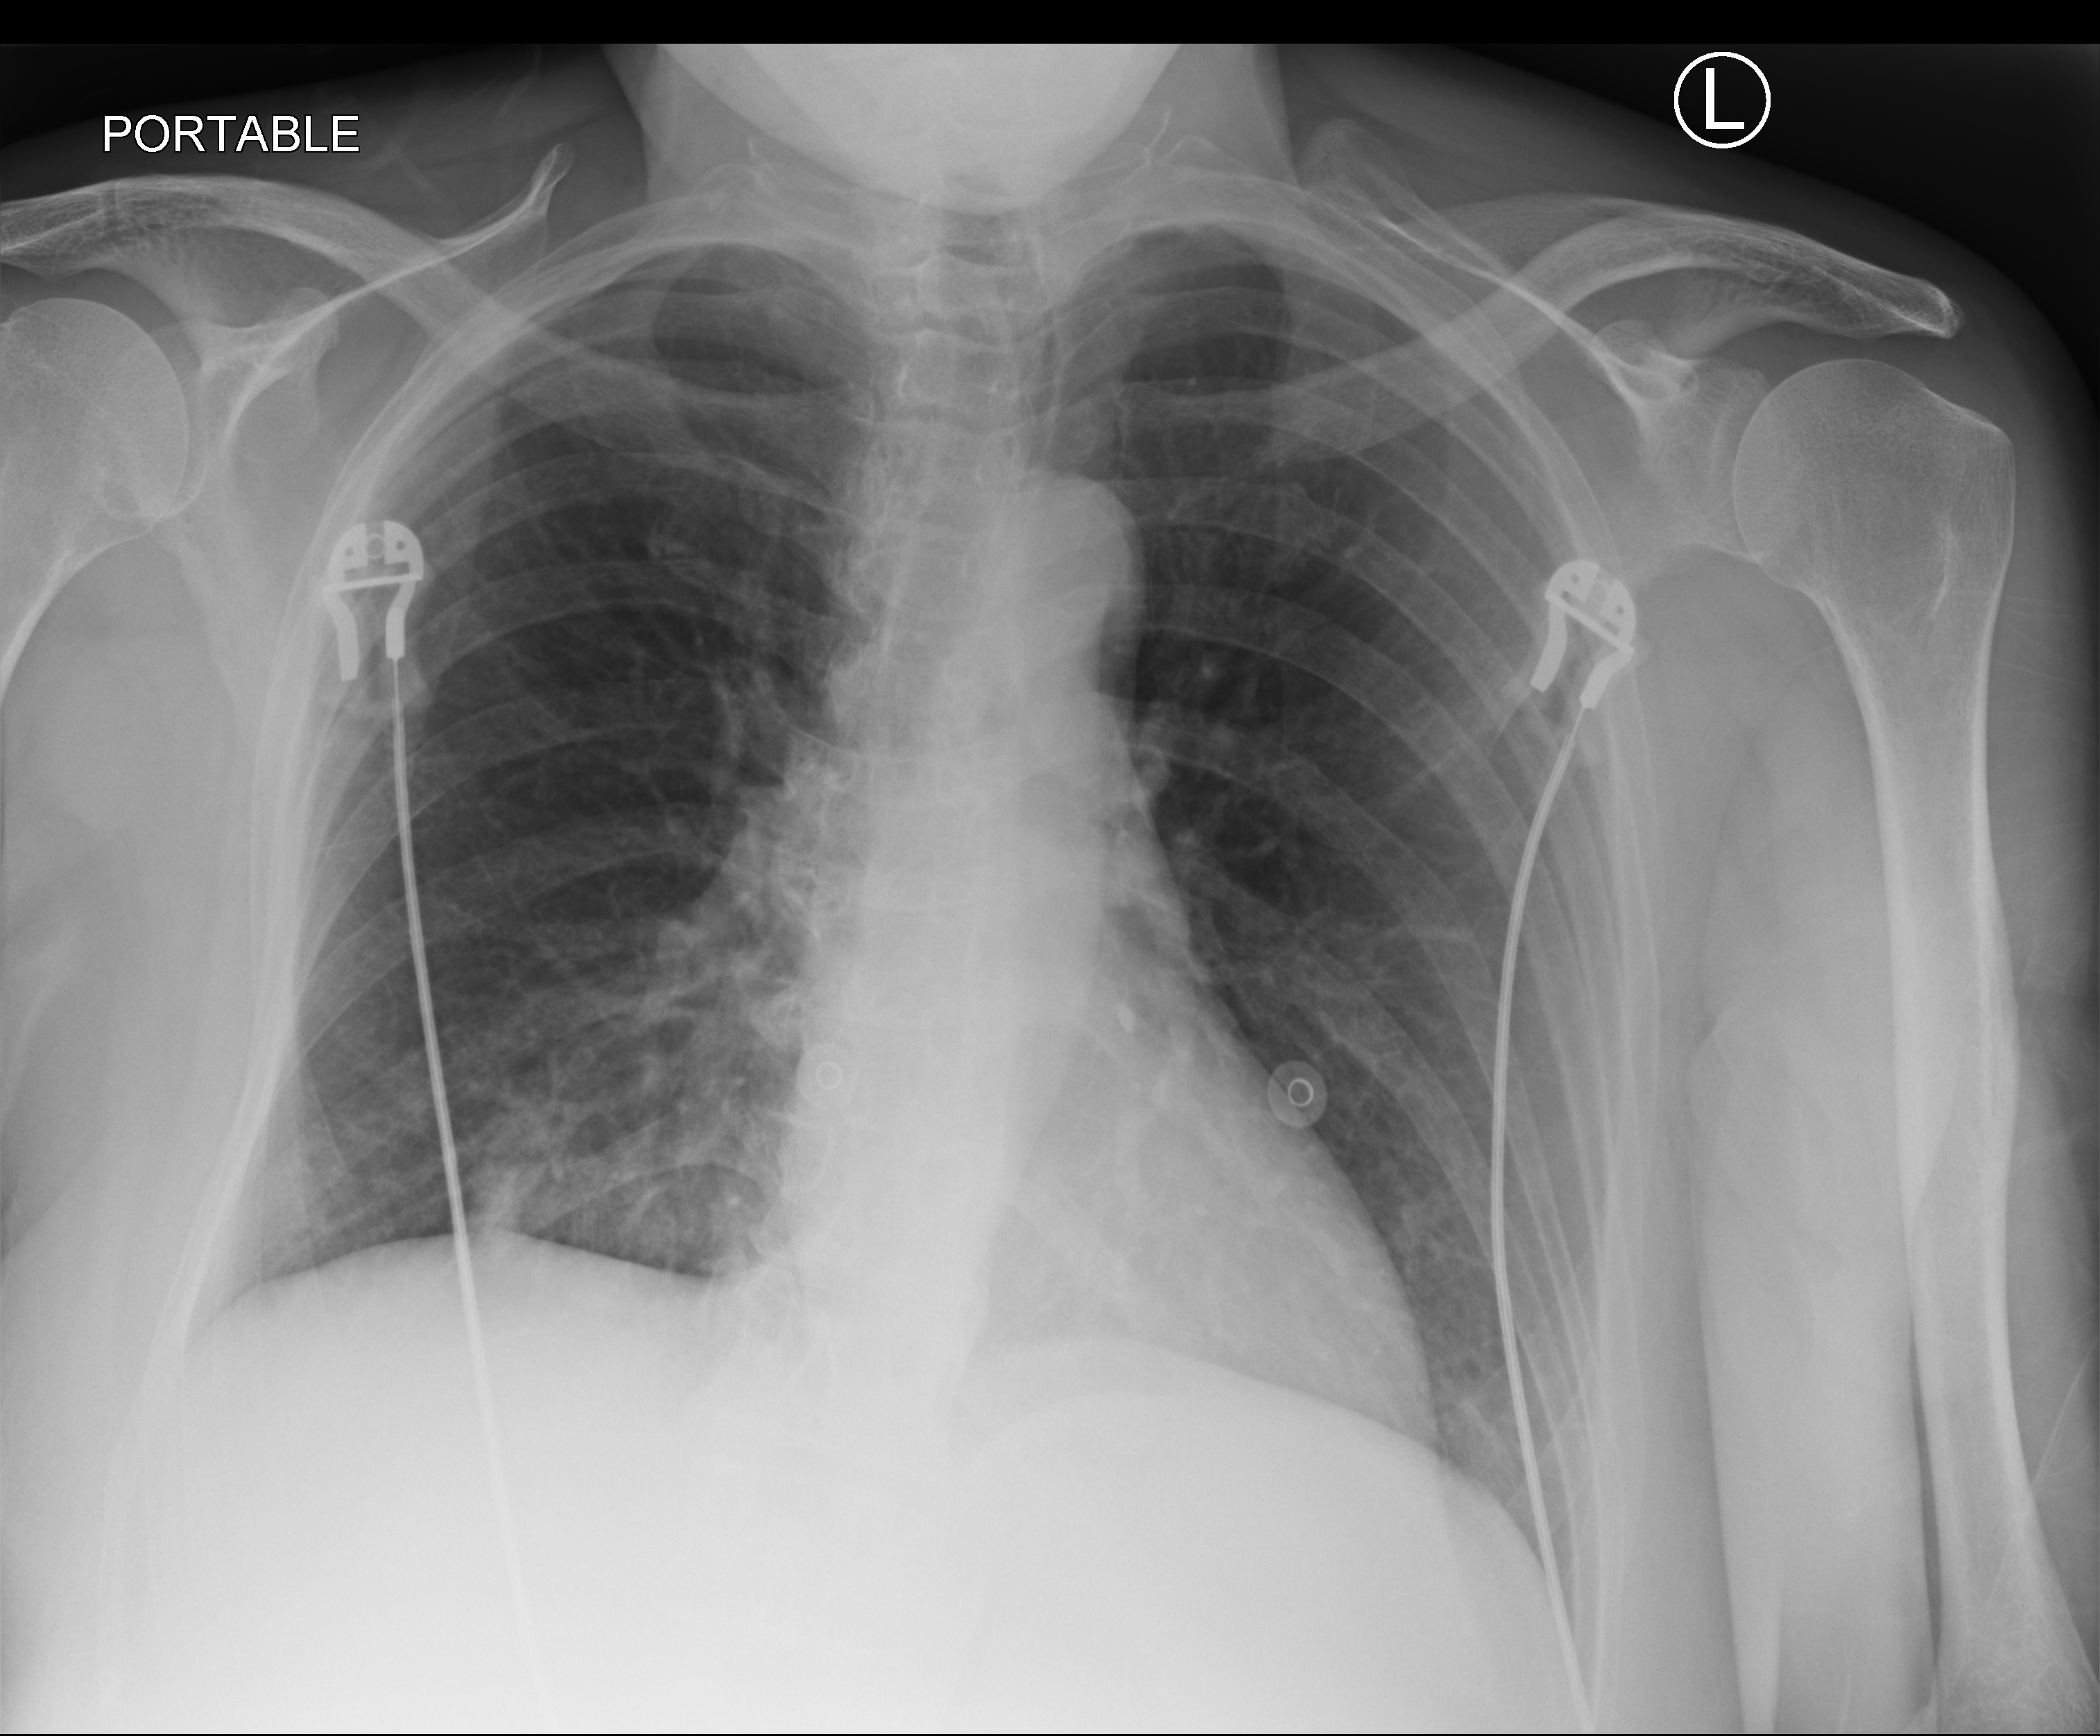
Chest X-ray (portable), anteroposterior (AP) projection. Female patient hospitalised with COVID-19, age 60–74 years.
From the hospital-stay record, not from the radiograph (when in the stay this image was taken is not recorded): diabetes (admission record): no.